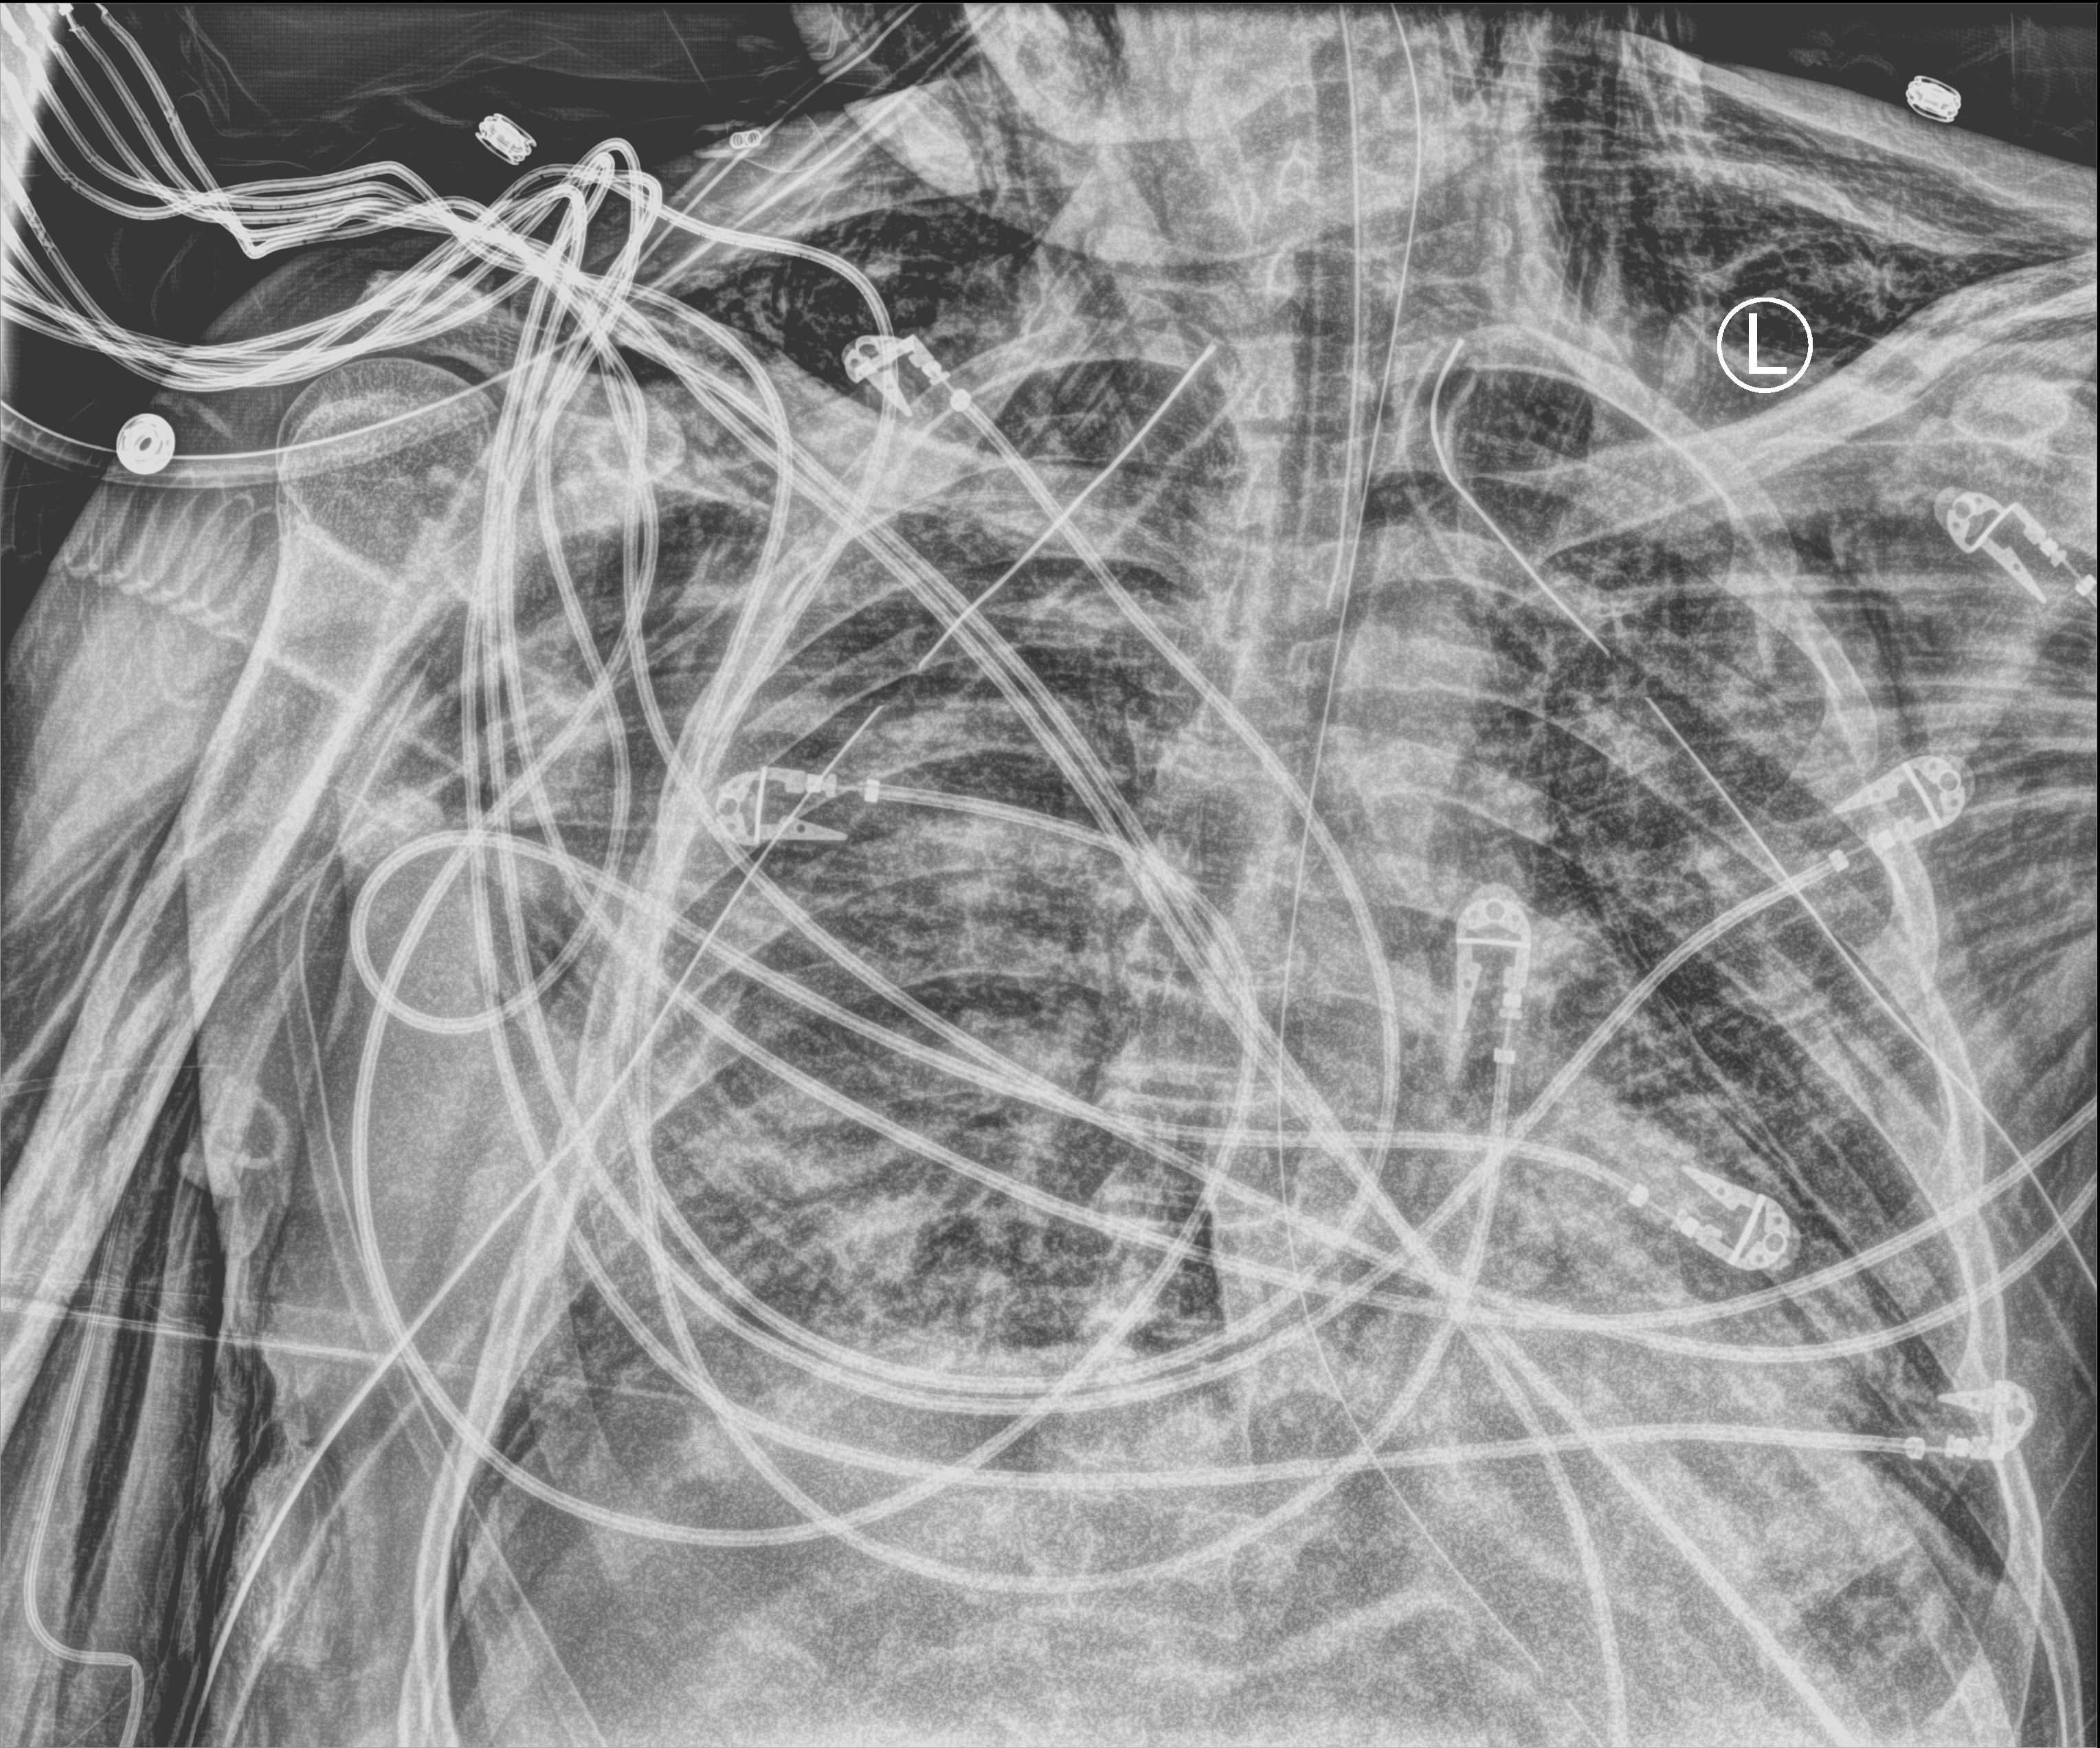
Portable chest radiograph. Patient hospitalised with COVID-19; male, aged 18–59 years.
Admission-level facts for this patient (not findings on this image; timing relative to this image not recorded): admitted to intensive care during this hospital stay: yes; smoking status (admission record): never.